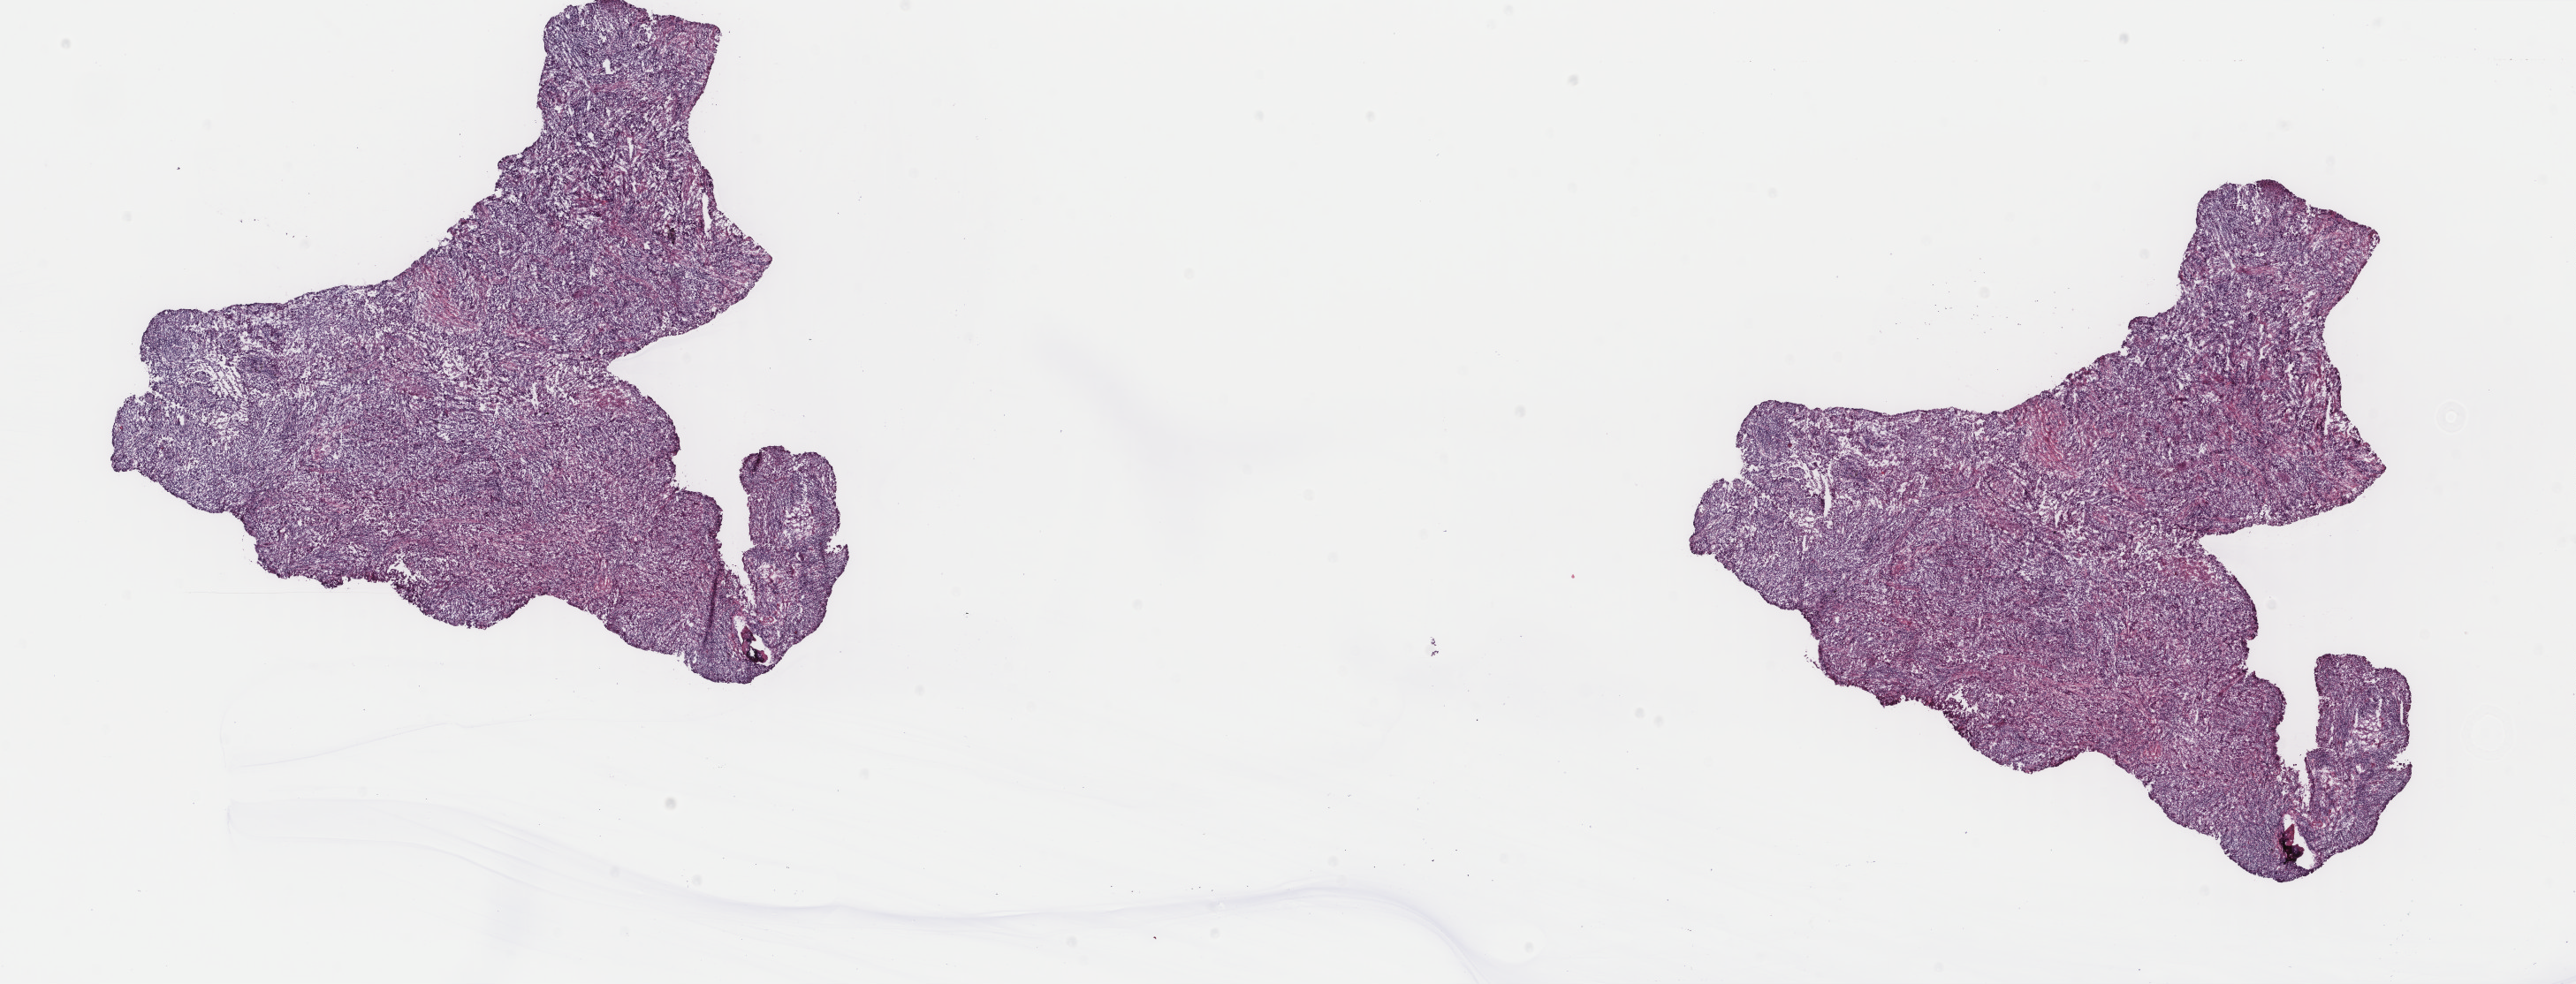
Digitized Hematoxylin and eosin (H&E) stained tissue section (whole slide) — shown as a low-resolution overview of the whole scanned area (about 23.1 x 8.8 mm). Frozen section from the top of the tissue portion. Lung, primary tumour sample. Patient: female, age at initial diagnosis 61 years. Composition of this section per pathologist review: tumour cells 60%, tumour nuclei 65%, normal cells 0%, stromal cells 30%, necrosis 10%. Inflammatory infiltration, as recorded: lymphocyte infiltration 15%, monocyte infiltration 5%, neutrophil infiltration 3%.
AJCC pathologic stage: IIA (7th edition). Histologic diagnosis: Squamous cell carcinoma, NOS.